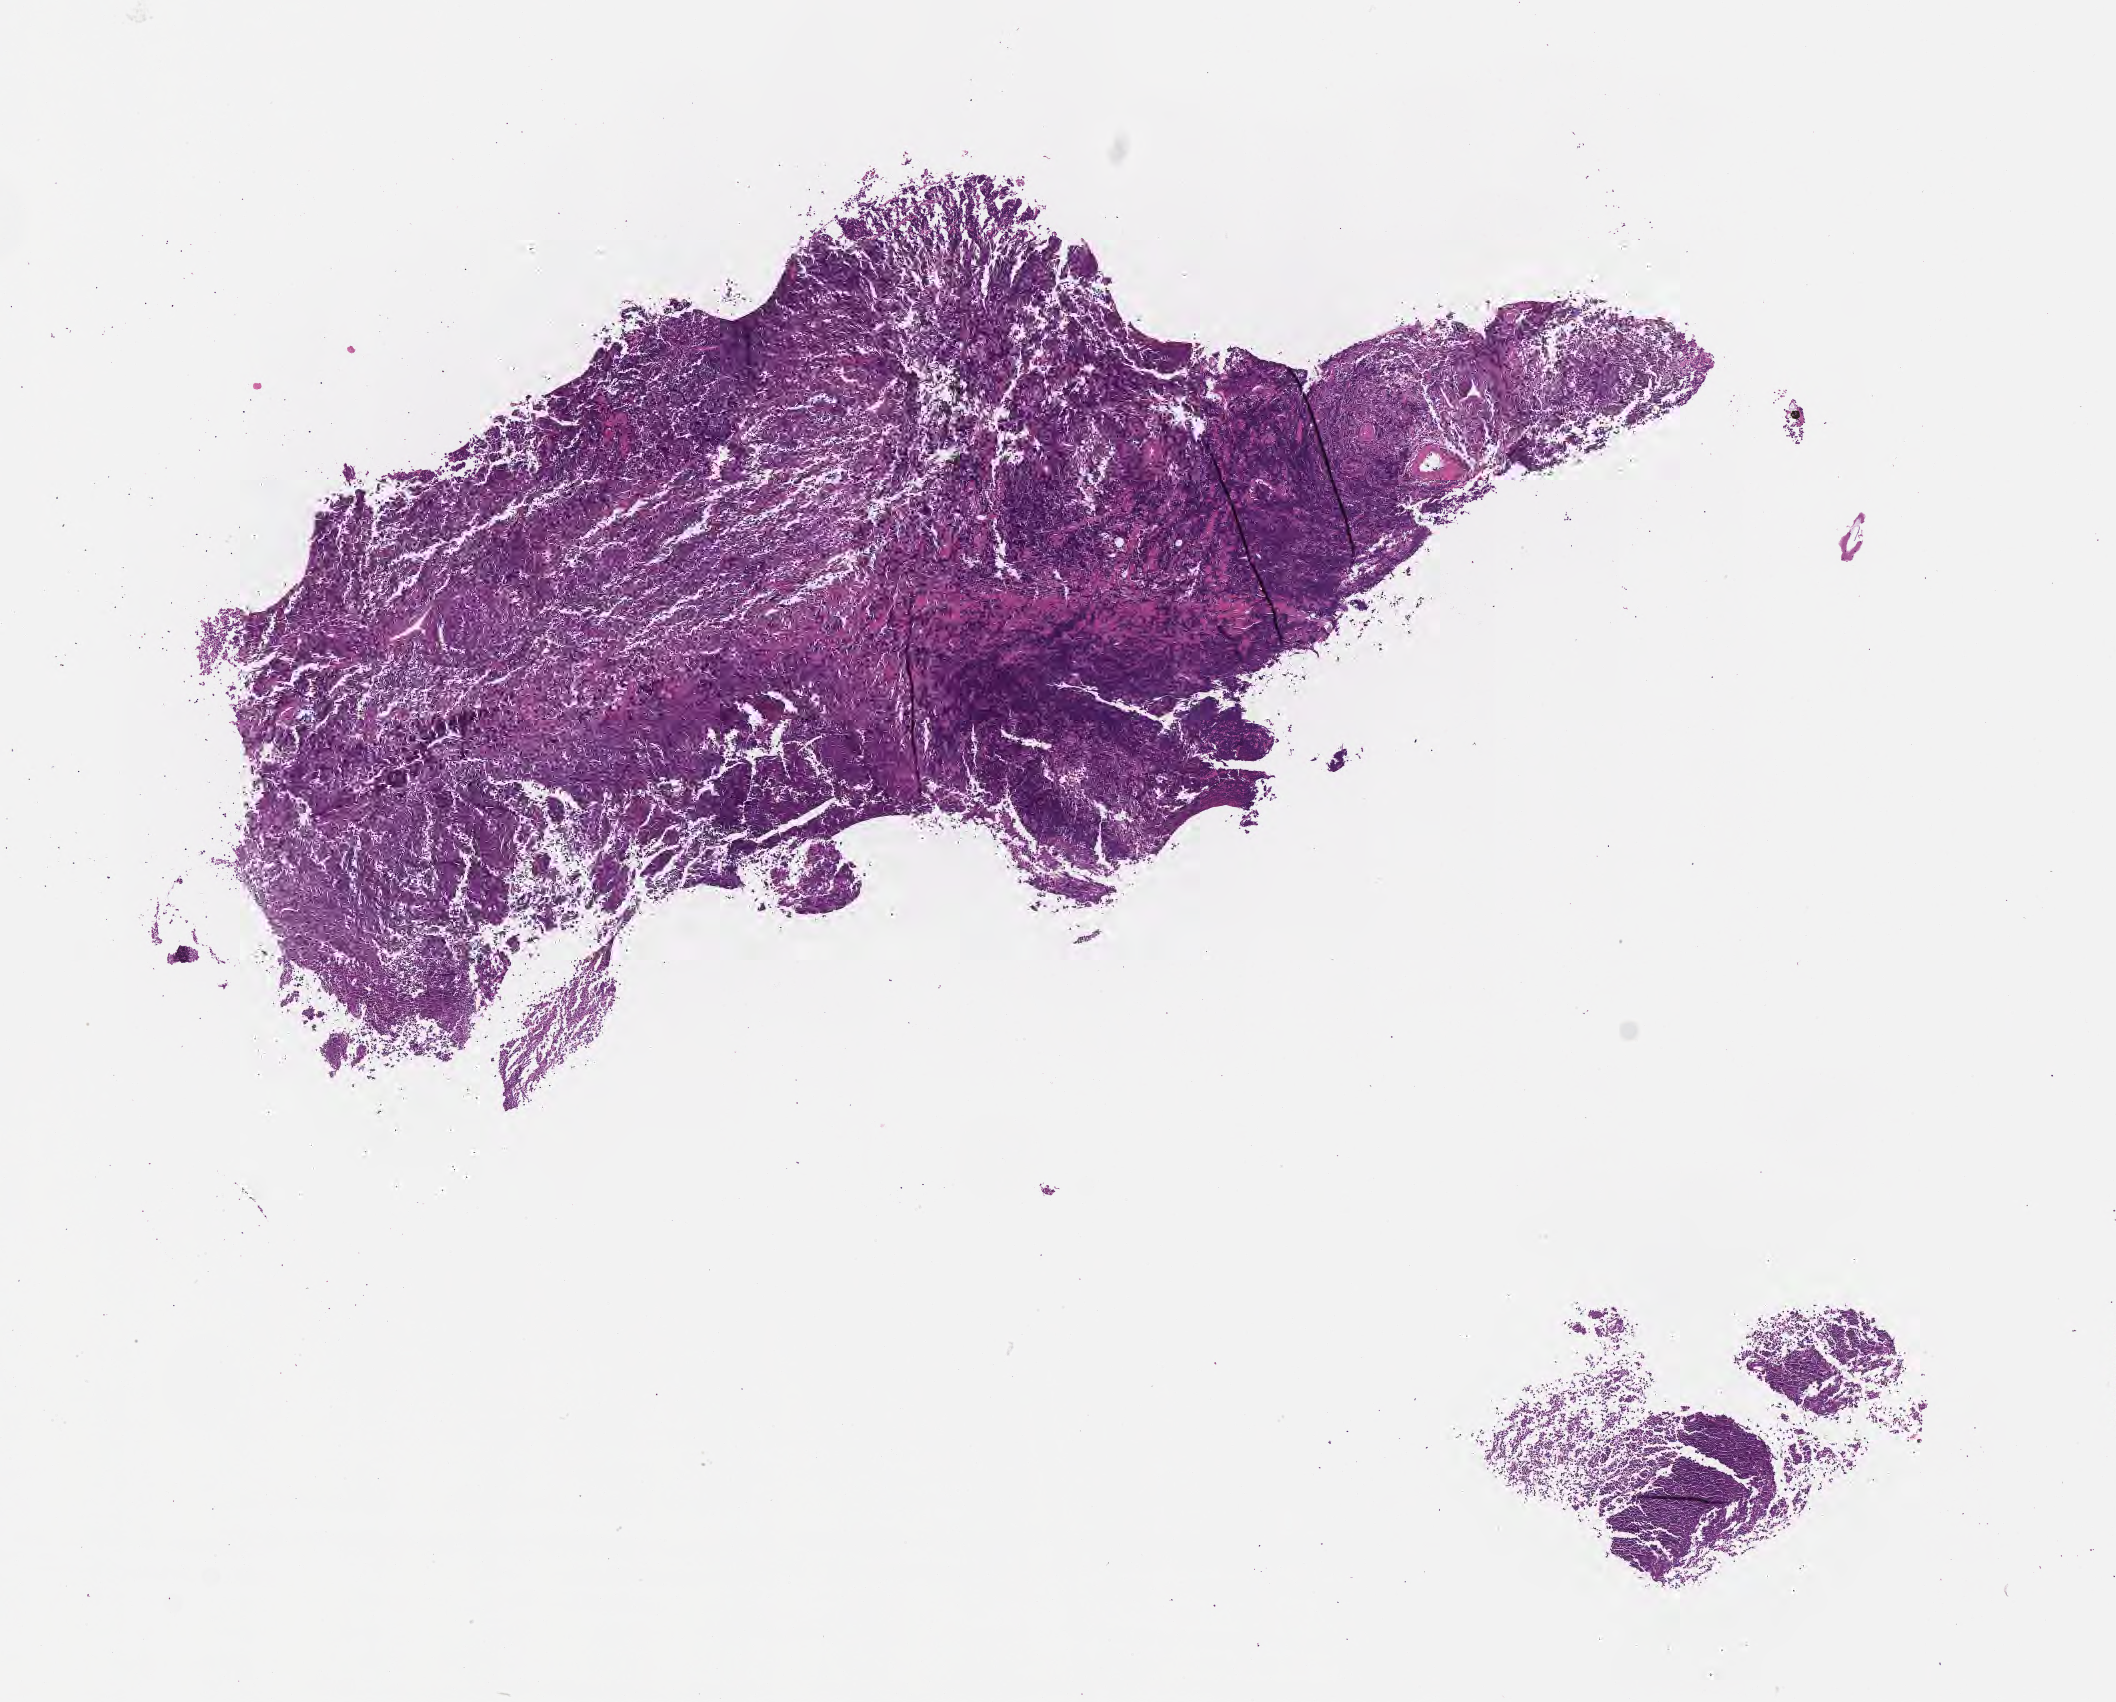
H&E whole-slide image, shown as a low-resolution overview of the whole scanned area (about 8.6 x 6.9 mm), formalin-fixed, paraffin-embedded (FFPE) tissue, specimen: primary tumor. Patient: male, age at initial diagnosis 3 years. Composition of this section per pathologist review: tumor cells 95%, tumor nuclei 95%, stromal cells 5%, necrosis 0%, normal cells 0%. Infiltration values recorded for this section: lymphocyte infiltration 80%, monocyte infiltration 10%, neutrophil infiltration 0%.
* Ann Arbor stage (patient): Stage IV
* histologic diagnosis: Burkitt lymphoma, NOS